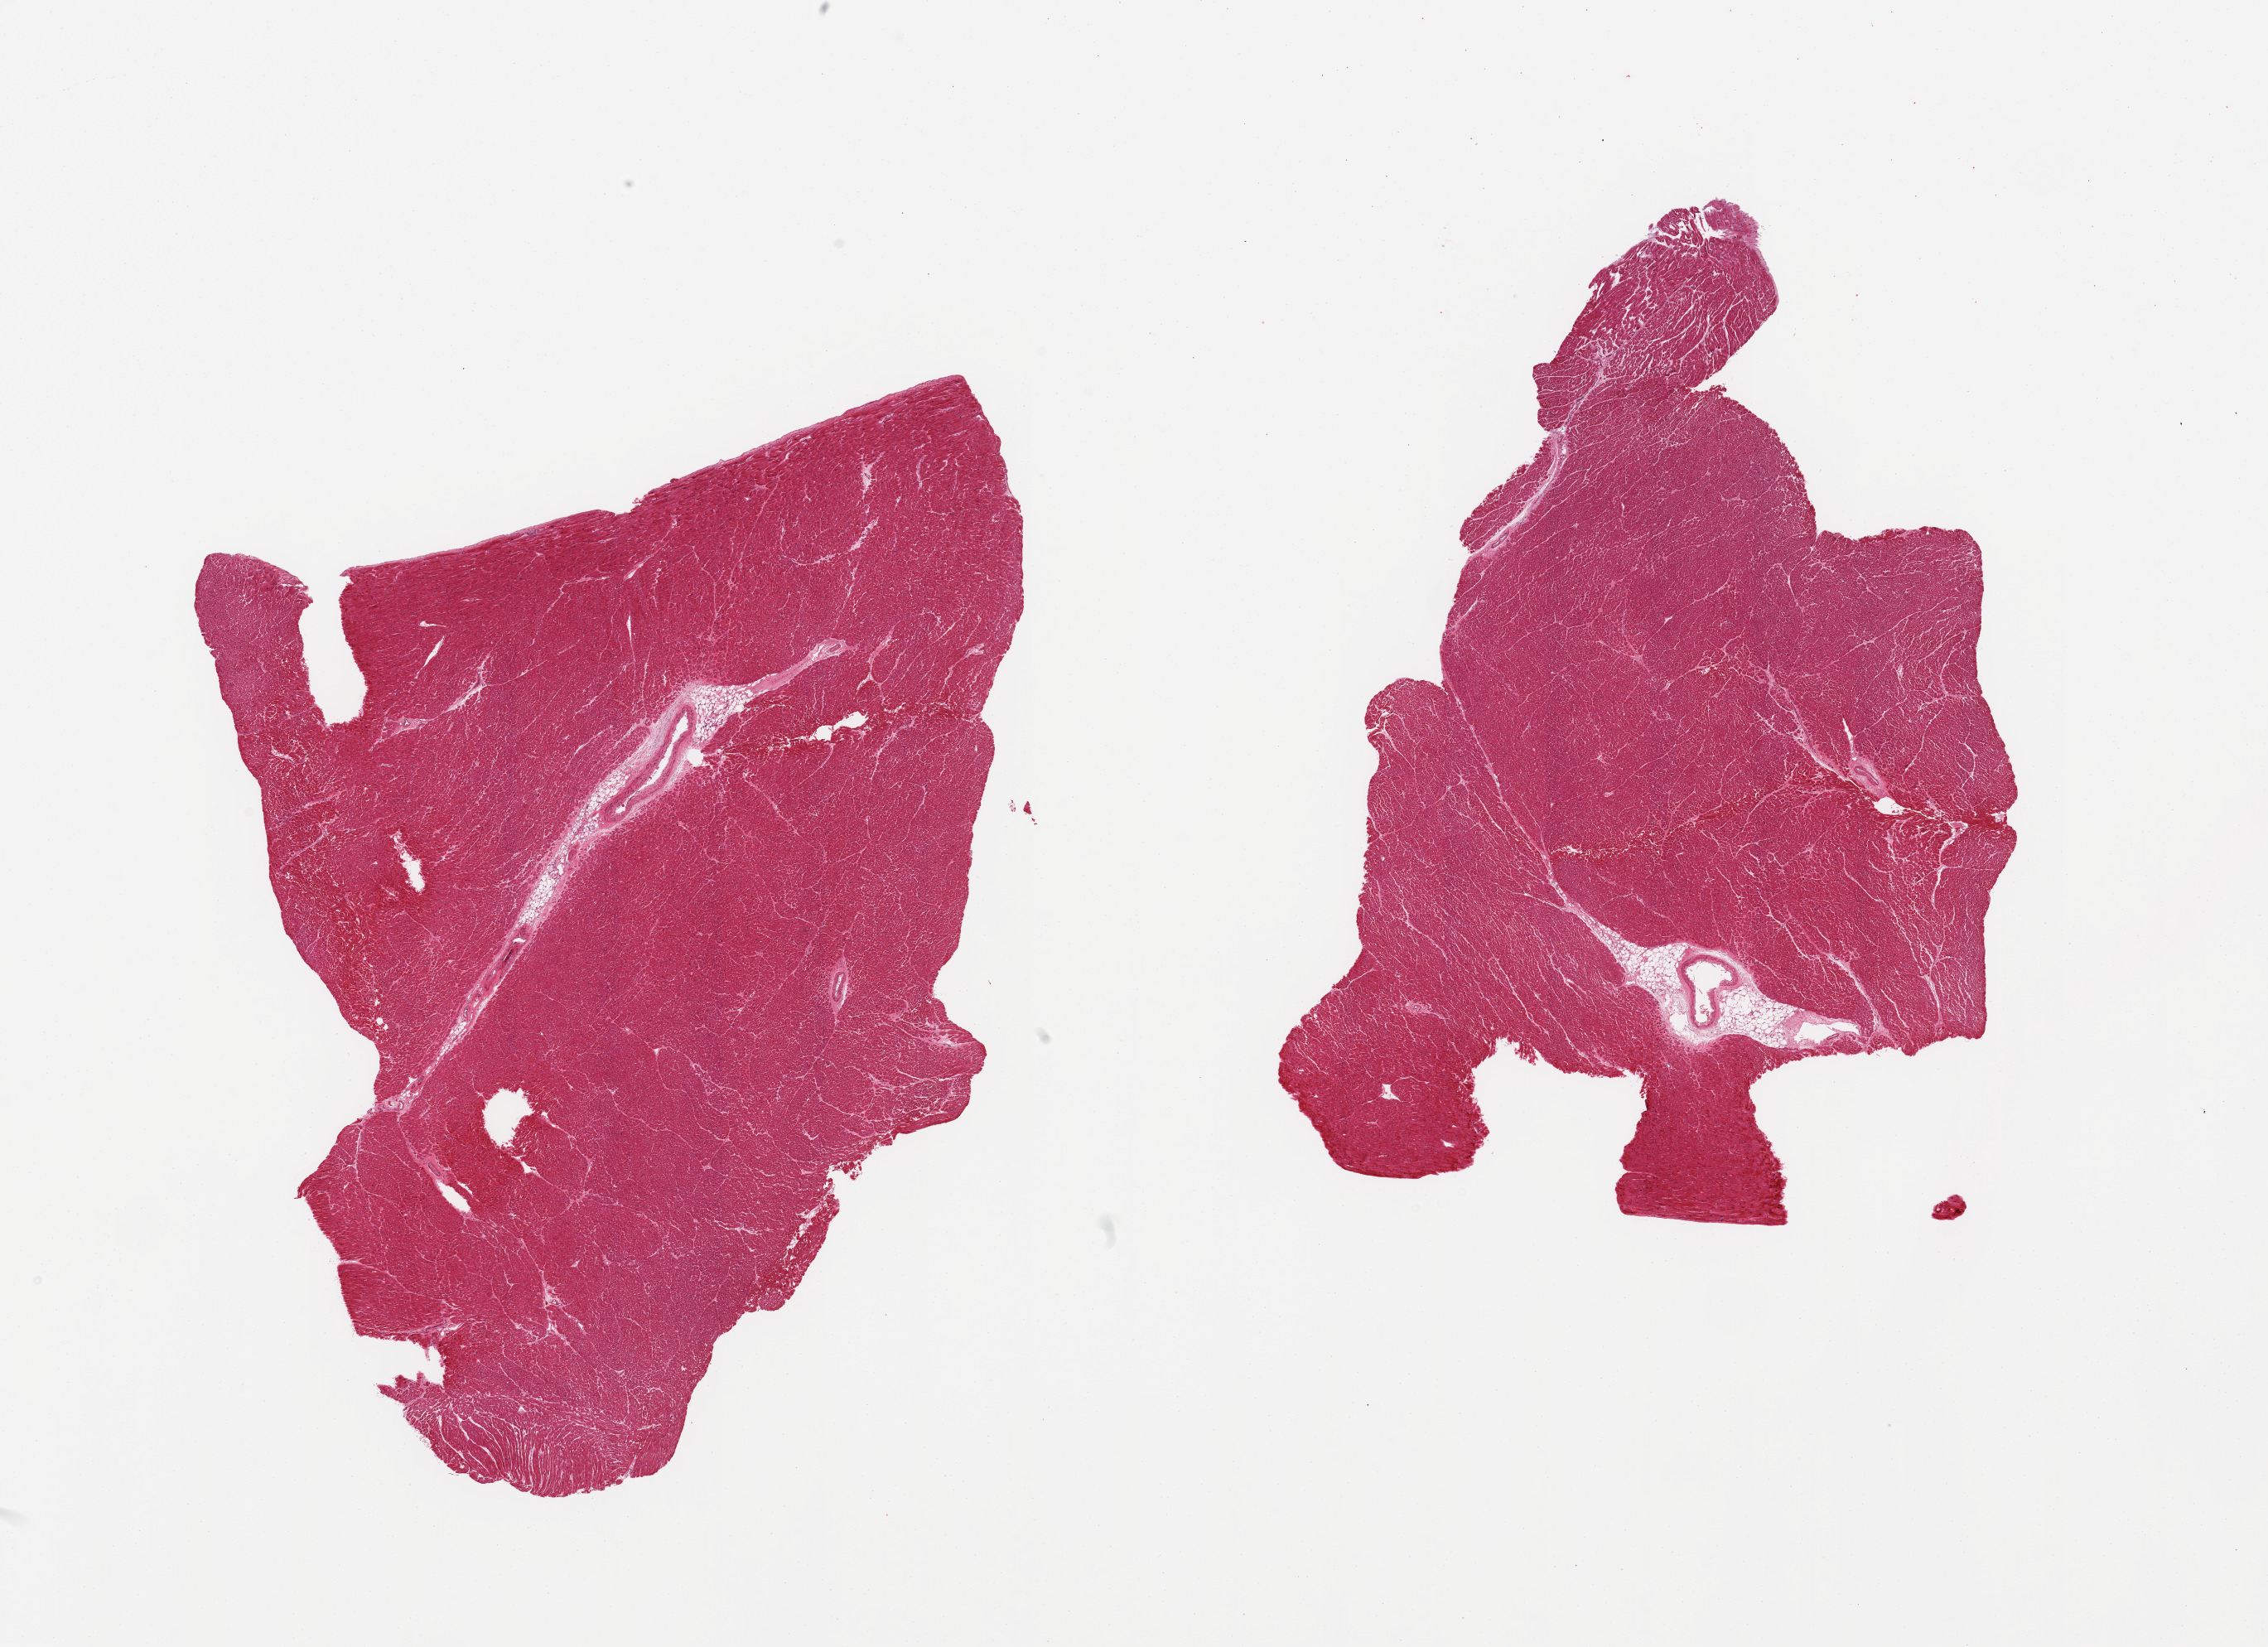
H&E whole-slide image — shown as a low-resolution overview of the whole scanned area (about 21.7 x 15.7 mm). PAXgene-fixed paraffin-embedded (PFPE) section. Sampled site (target tissue): heart. Tissue donor sample. Male donor.
• pathologist's review note for this sample: 2 pieces; intramuscular vessels surrounded by ~1mm rim of adipose tissue; accentuation of interstitial connective tissue